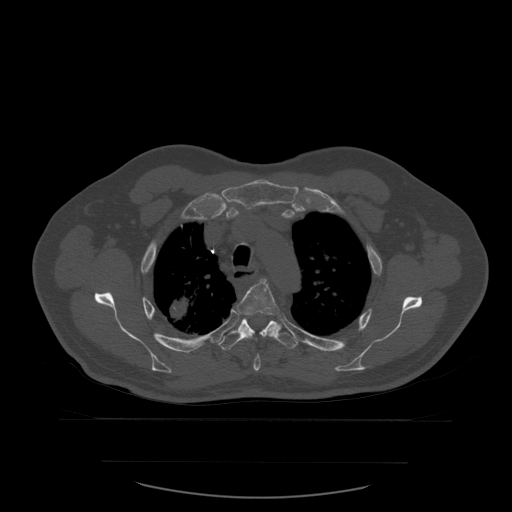
CT including the spine, one axial slice; slice 435 of 590 in the series (ordered by position); bone window (W 1800 / L 400 HU); 1.25 mm slice thickness; 512 × 512 image matrix. Patient age 71 years. Case-level facts recorded for this patient, not image findings: primary cancer: lung.
Annotated regions visible in this slice (semi-automatic segmentation, software-assisted and operator-edited):
- T4 vertebra: bounding box <237,279,281,372> (left, top, right, bottom; pixels)
- T5 vertebra: <218,314,299,351>